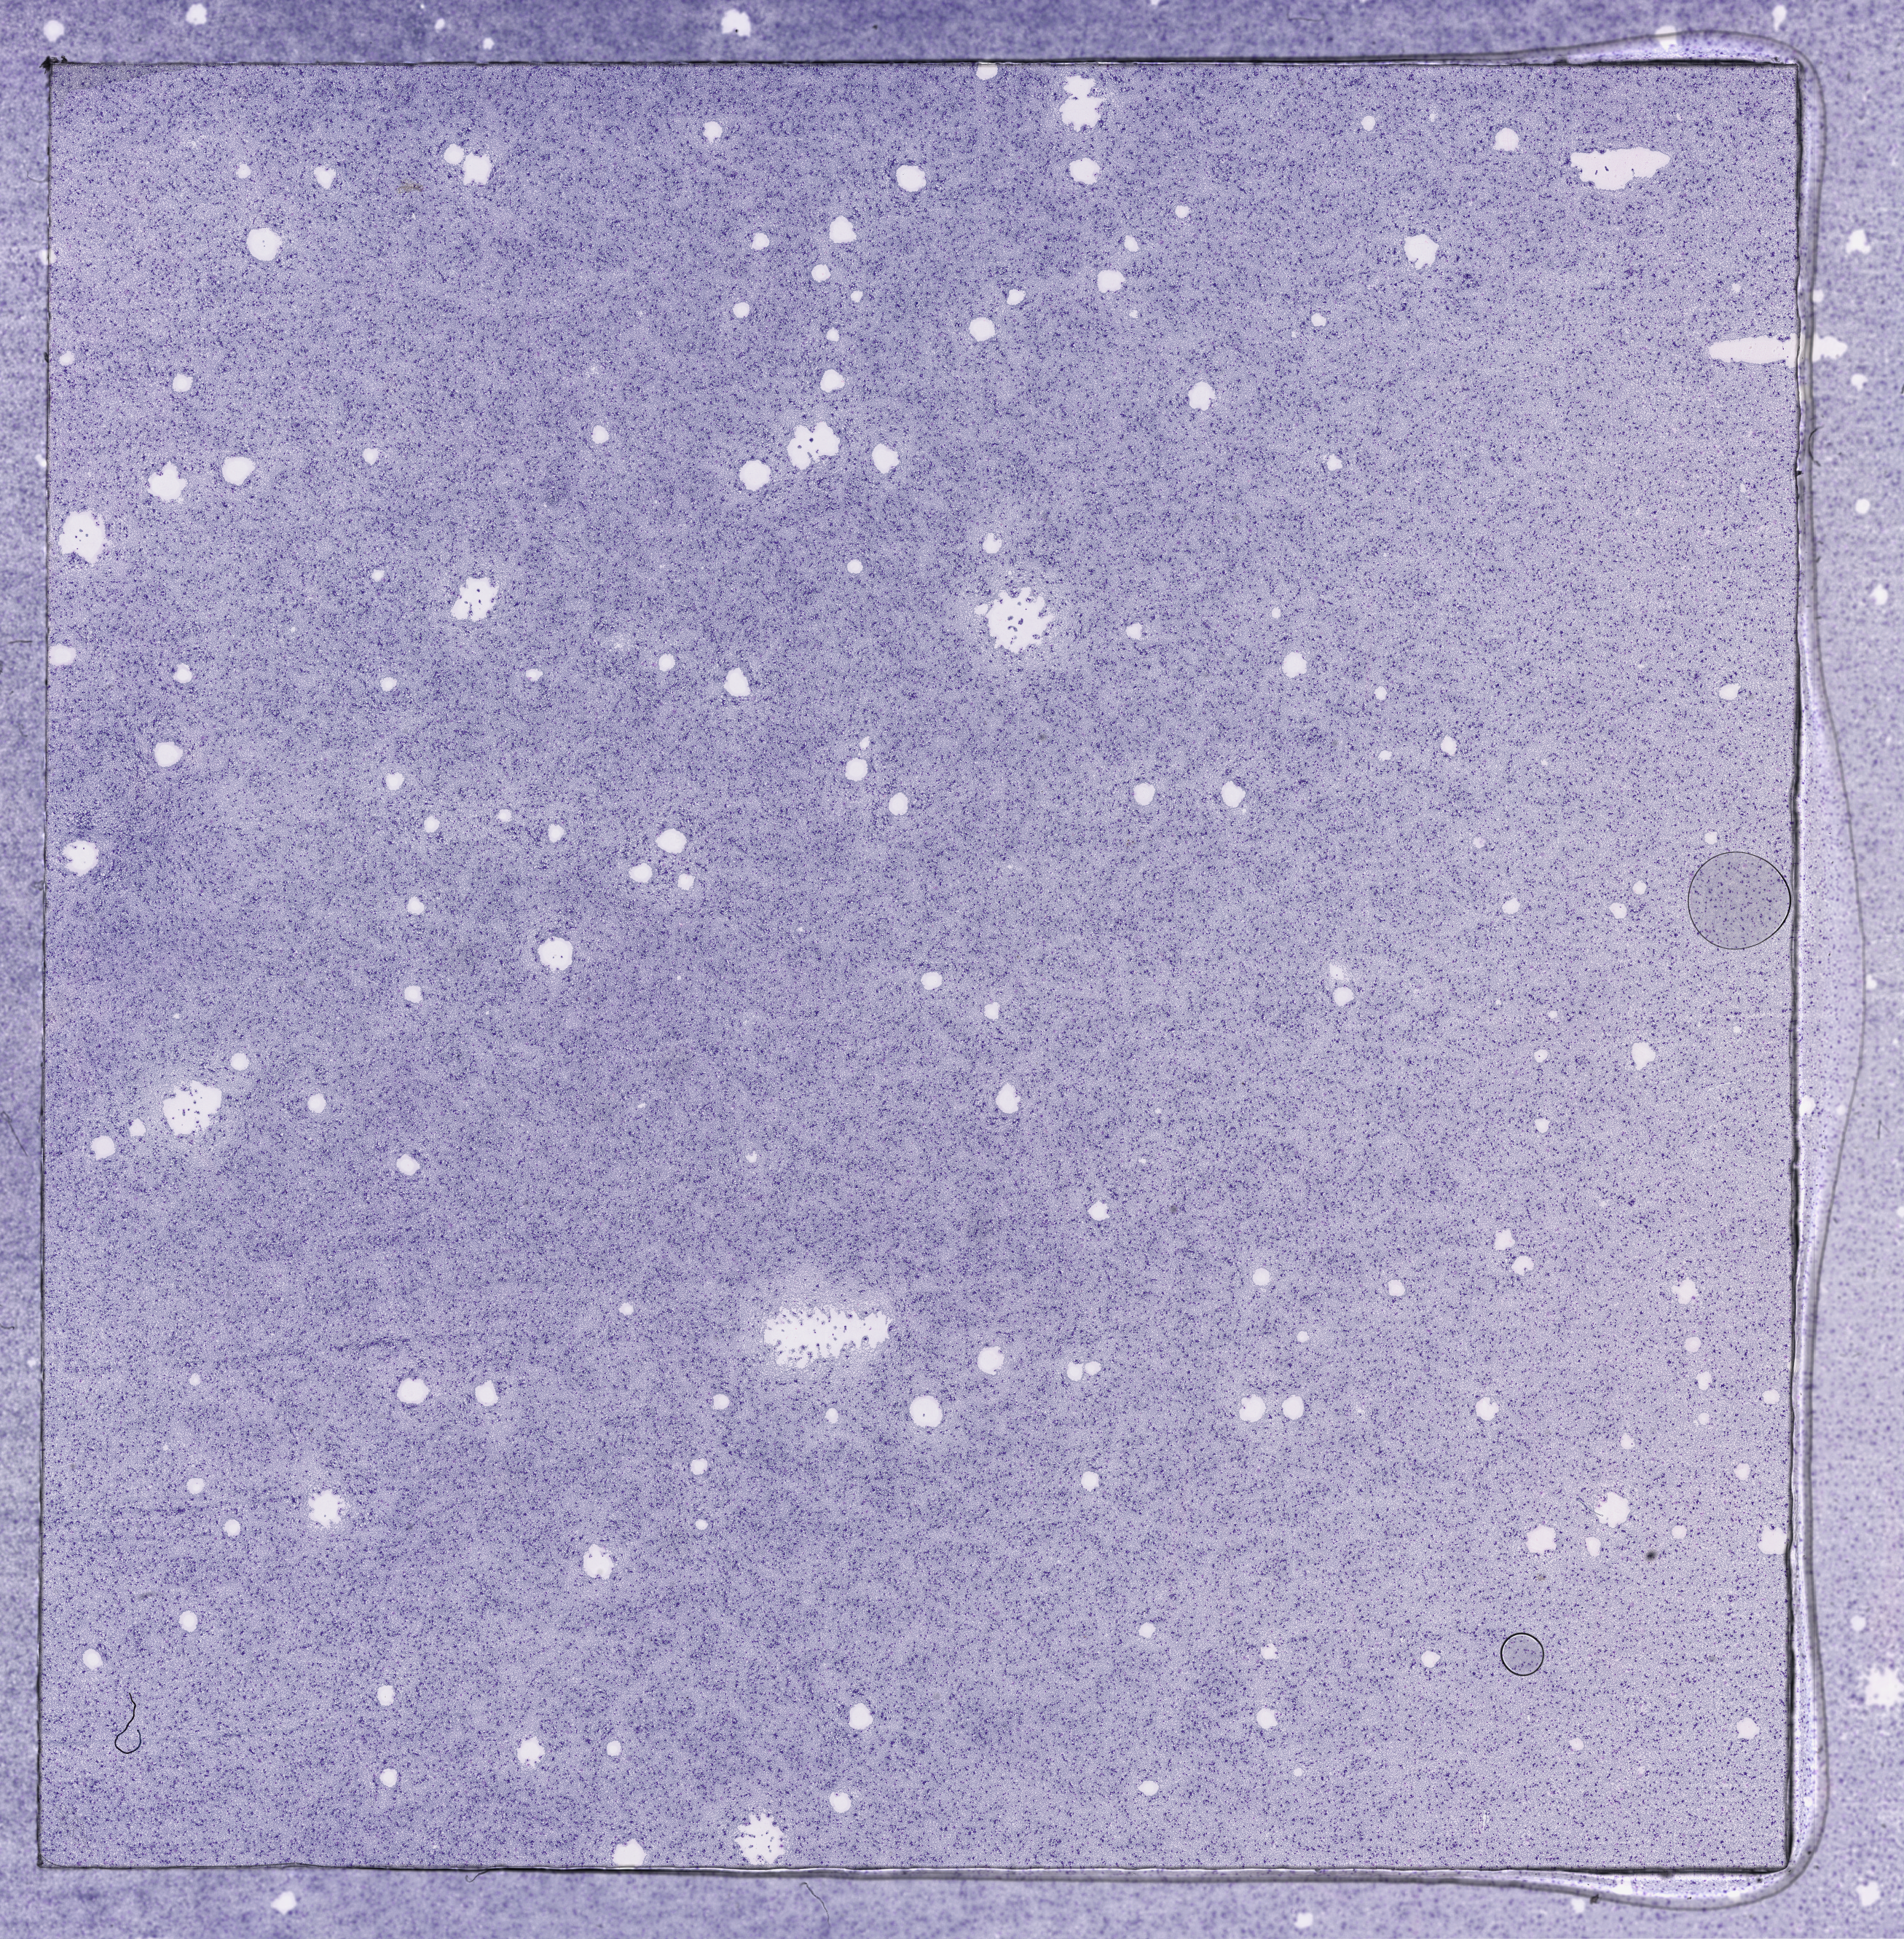
Digitized H&E tissue section (whole slide), low-resolution overview of the scanned area, about 21.1 x 21.5 mm; bone marrow (leukaemic) sample. 65-year-old female patient. Blasts: 90%.
- diagnosis: Acute Myeloid Leukemia
- WHO classification: Acute myelomonocytic leukemia
- FAB classification: M4